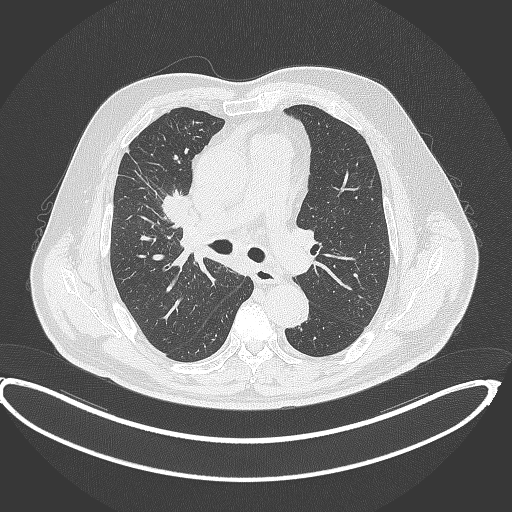
Chest CT, one axial slice; position 255 of 390 along the scan axis; reconstruction kernel B70f; 120 kVp; lung window (W 1500 / L -600 HU); 1 mm slice thickness; 512 × 512 image matrix, field of view 448 × 448 mm. Patient: male, 62 years. From the clinical record (not read from this slice): clinical TNM (as recorded): T1c N3 M1c.
Annotated regions visible in this slice (bounding box drawn by a radiologist):
- lung tumour (recorded histology: adenocarcinoma): box from (x=159, y=195) to (x=191, y=222) px